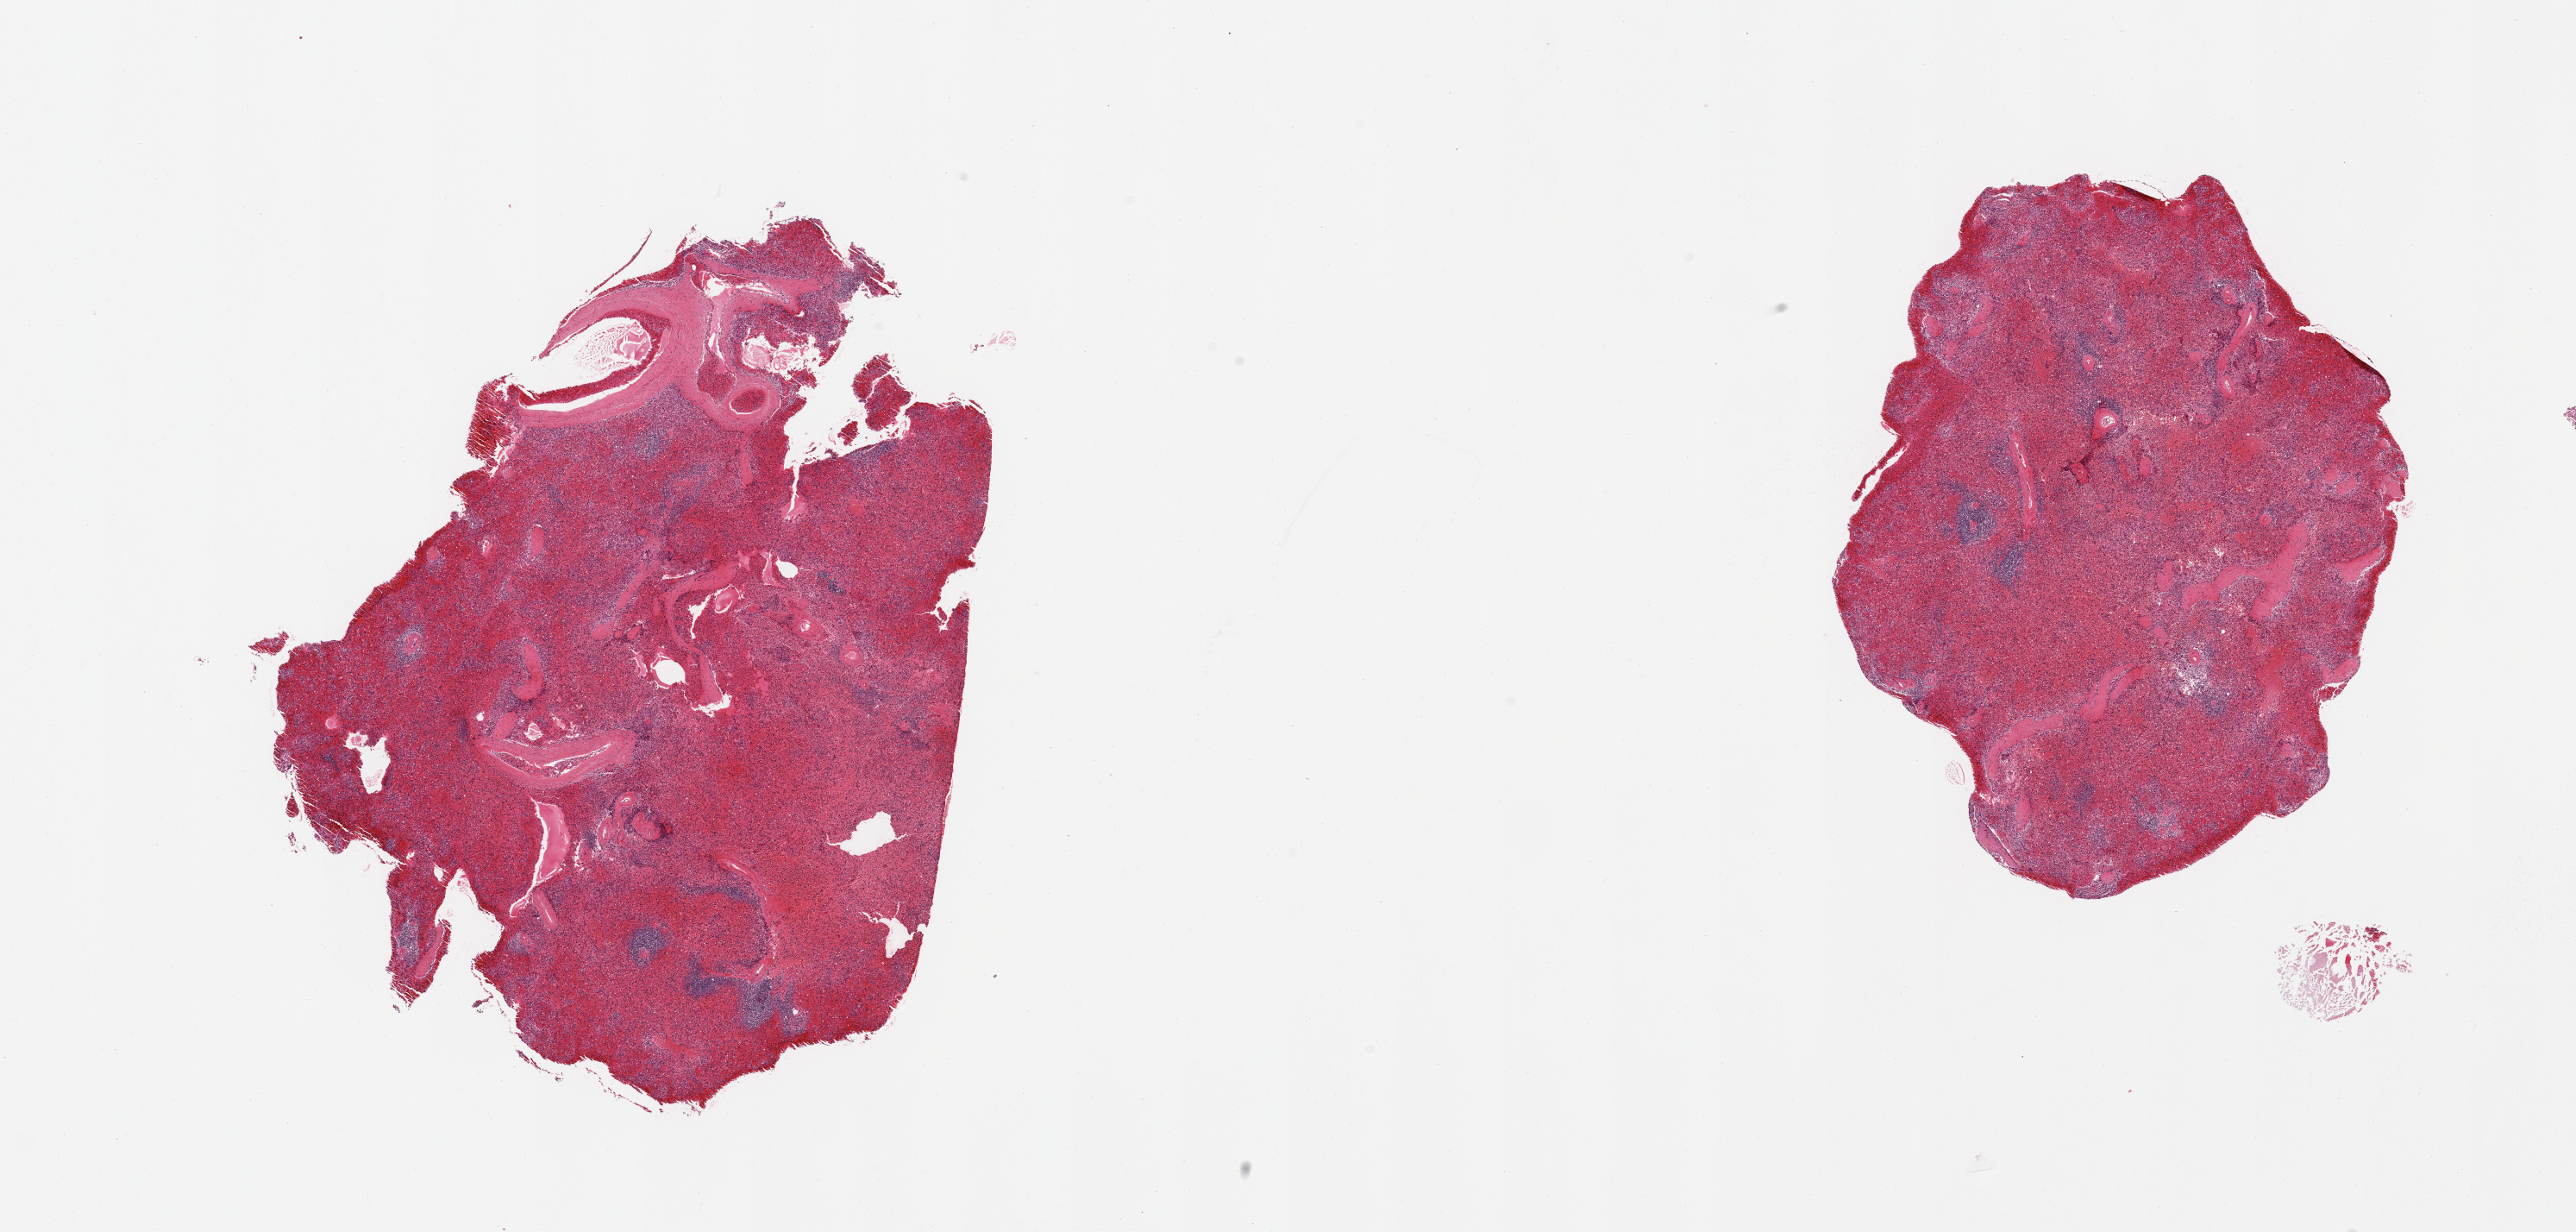
Digitized haematoxylin and eosin-stained section, brightfield — shown as a low-resolution overview of the whole scanned area (about 23.6 x 11.3 mm, from a 20x scan), PAXgene-fixed, paraffin-embedded tissue, target tissue: spleen, tissue donor sample. Donor: male.
Reviewer comment on this tissue sample: 2 pieces; moderate congestion.